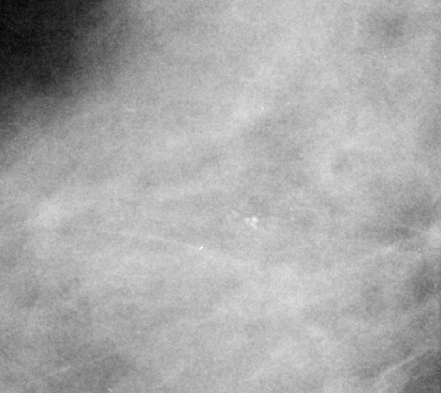
Cropped region of a digitized screen-film mammogram centred on a radiologist-marked abnormality; right breast; CC view; BI-RADS breast density category 3 (scale 1–4).
Marked abnormality: calcifications, morphology amorphous, distribution clustered; BI-RADS assessment category 4; subtlety rating 3 on a 1 (subtle) to 5 (obvious) scale; pathology (as recorded): malignant.